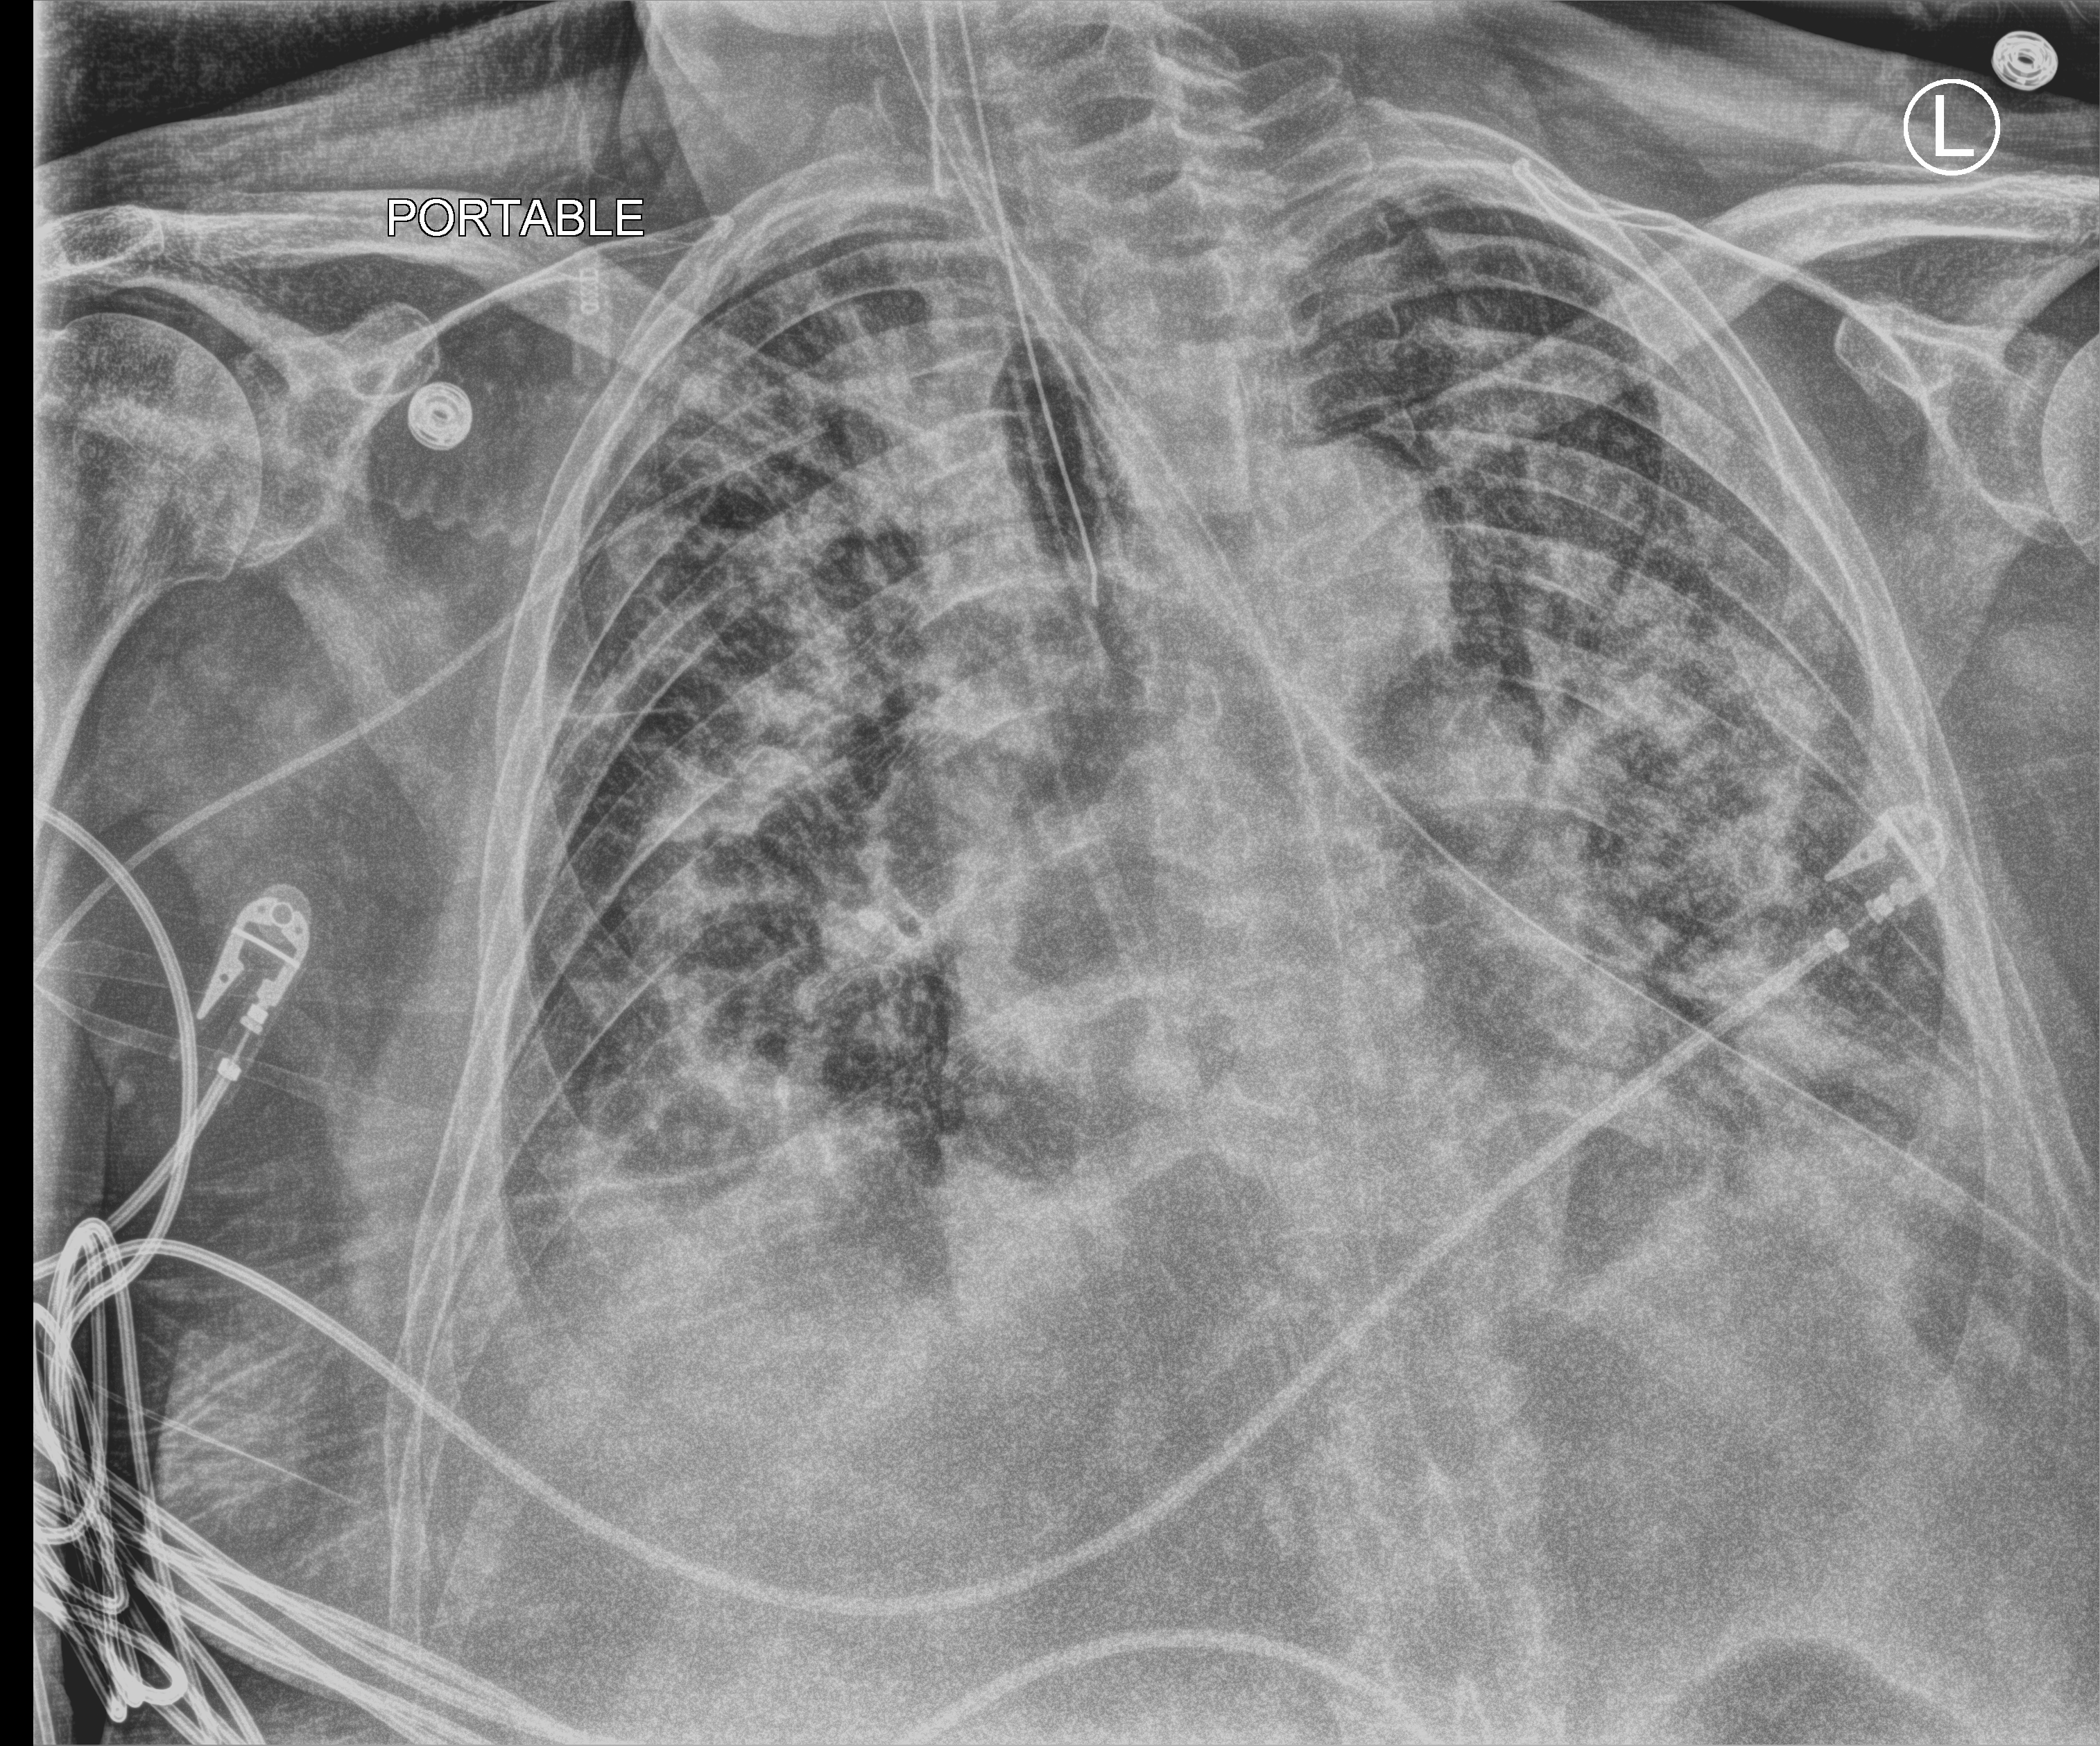
Chest X-ray (portable), anteroposterior (AP) projection. Patient hospitalised with COVID-19; male, aged 60–74 years.
Hospital-stay facts (about this admission, not read from this image; timing relative to this image not recorded): admitted to intensive care during this hospital stay: yes; hypertension (admission record): no; mechanically ventilated during this hospital stay: yes.